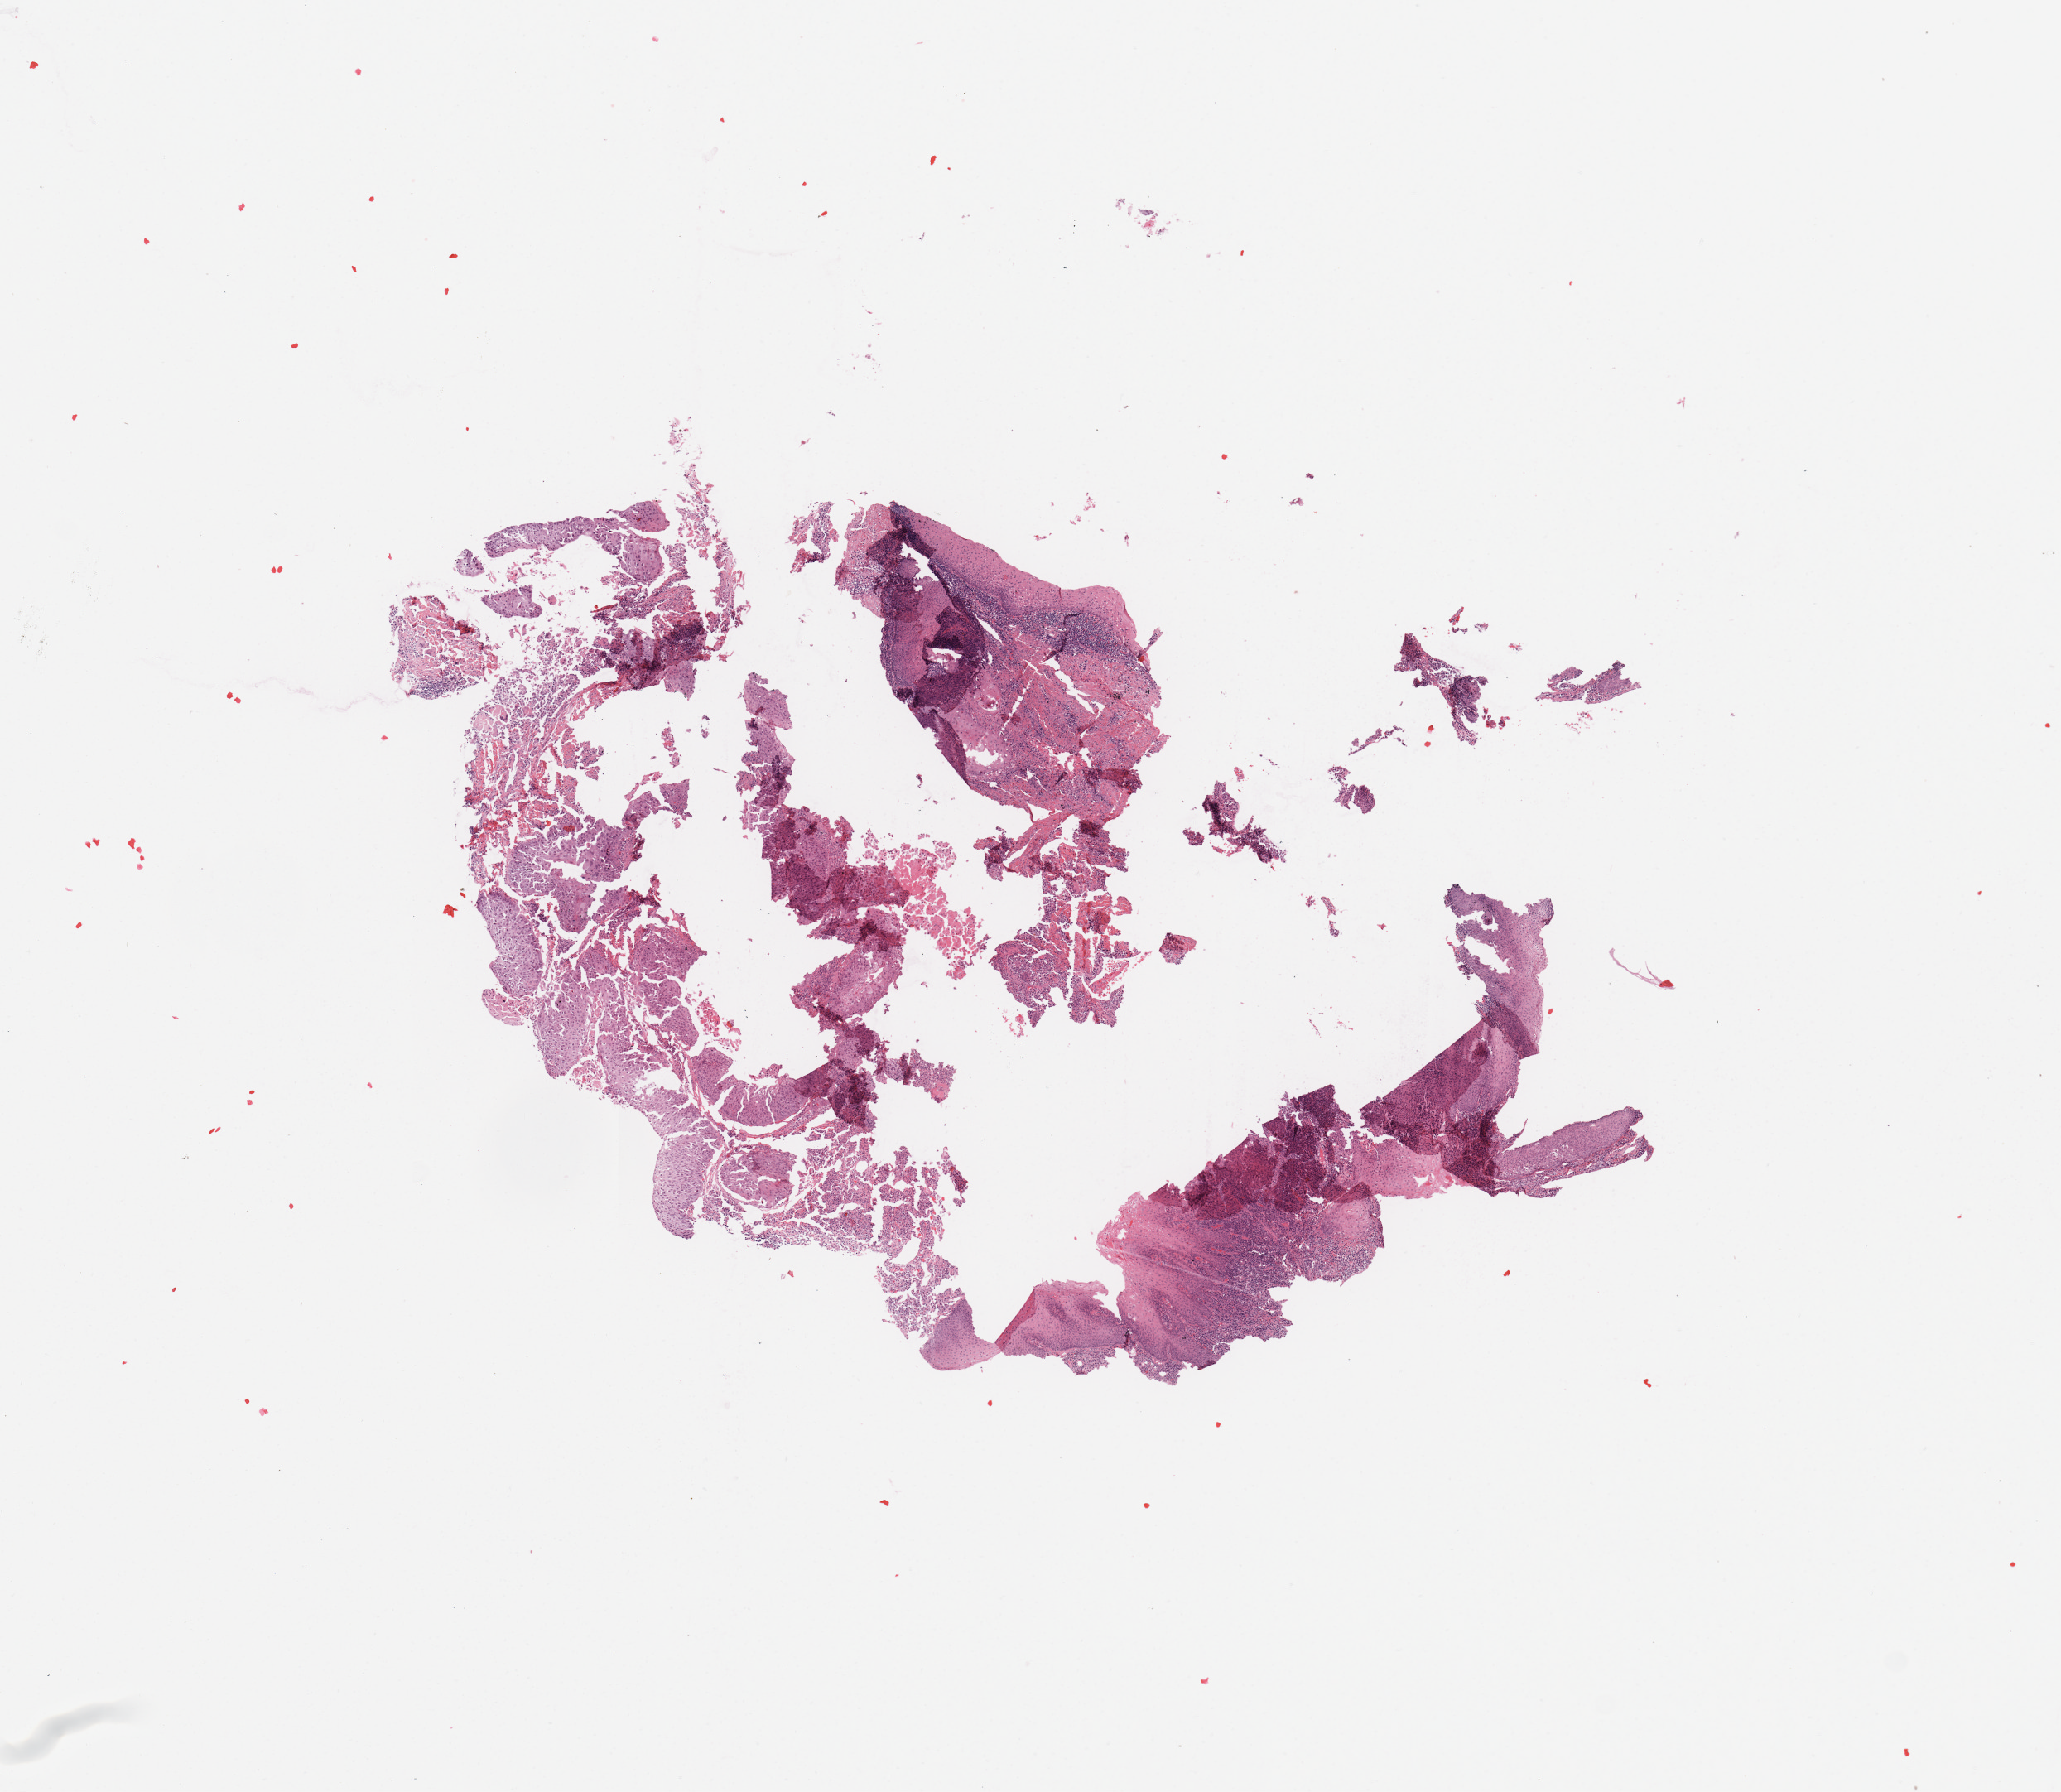
H&E whole-slide image — shown as a low-resolution overview of the whole scanned area (about 9.8 x 8.6 mm, from a 20x scan); tumour tissue sample, sampled site: larynx. Patient: male, age 55 years. Histologic grade: G1 (well differentiated). Pathologist review of this section (percent, as recorded): tumour nuclei 80%, necrosis 10%.
Primary tumour site (as recorded): larynx. Diagnosis: Squamous cell carcinoma, NOS (larynx, NOS). AJCC pathologic stage: IVA.